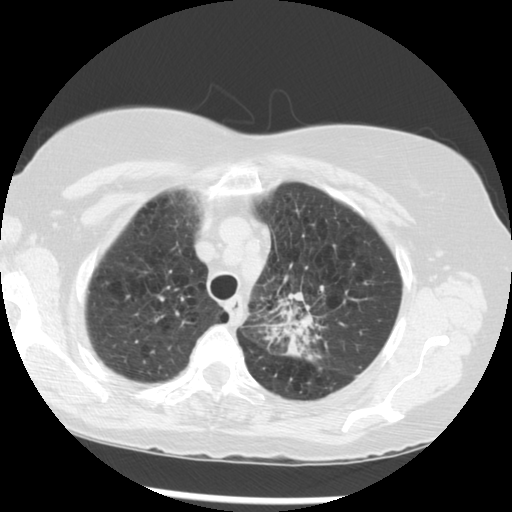
Chest CT (low-dose screening protocol), one axial image. Third screening round (two years after baseline). Lung window (W 1500 / L -600 HU). Female participant, aged 70 years at enrolment.
Lesion marked by an expert reader, box from (x=257, y=278) to (x=353, y=367) px. Screening reader's record for this exam (one nodule recorded; not confirmed to be the boxed lesion): non-calcified nodule or mass ≥4 mm, left upper lobe, 32 × 26 mm, spiculated (stellate) margins, soft tissue attenuation, pre-existing on the prior screen: yes; interval growth: yes. Official screen result: positive, other. Participant outcome: lung cancer diagnosed 24 days after this screen — neoplasm, malignant, left upper lobe, stage IIIB (AJCC 6th edition), 40 mm at pathology.